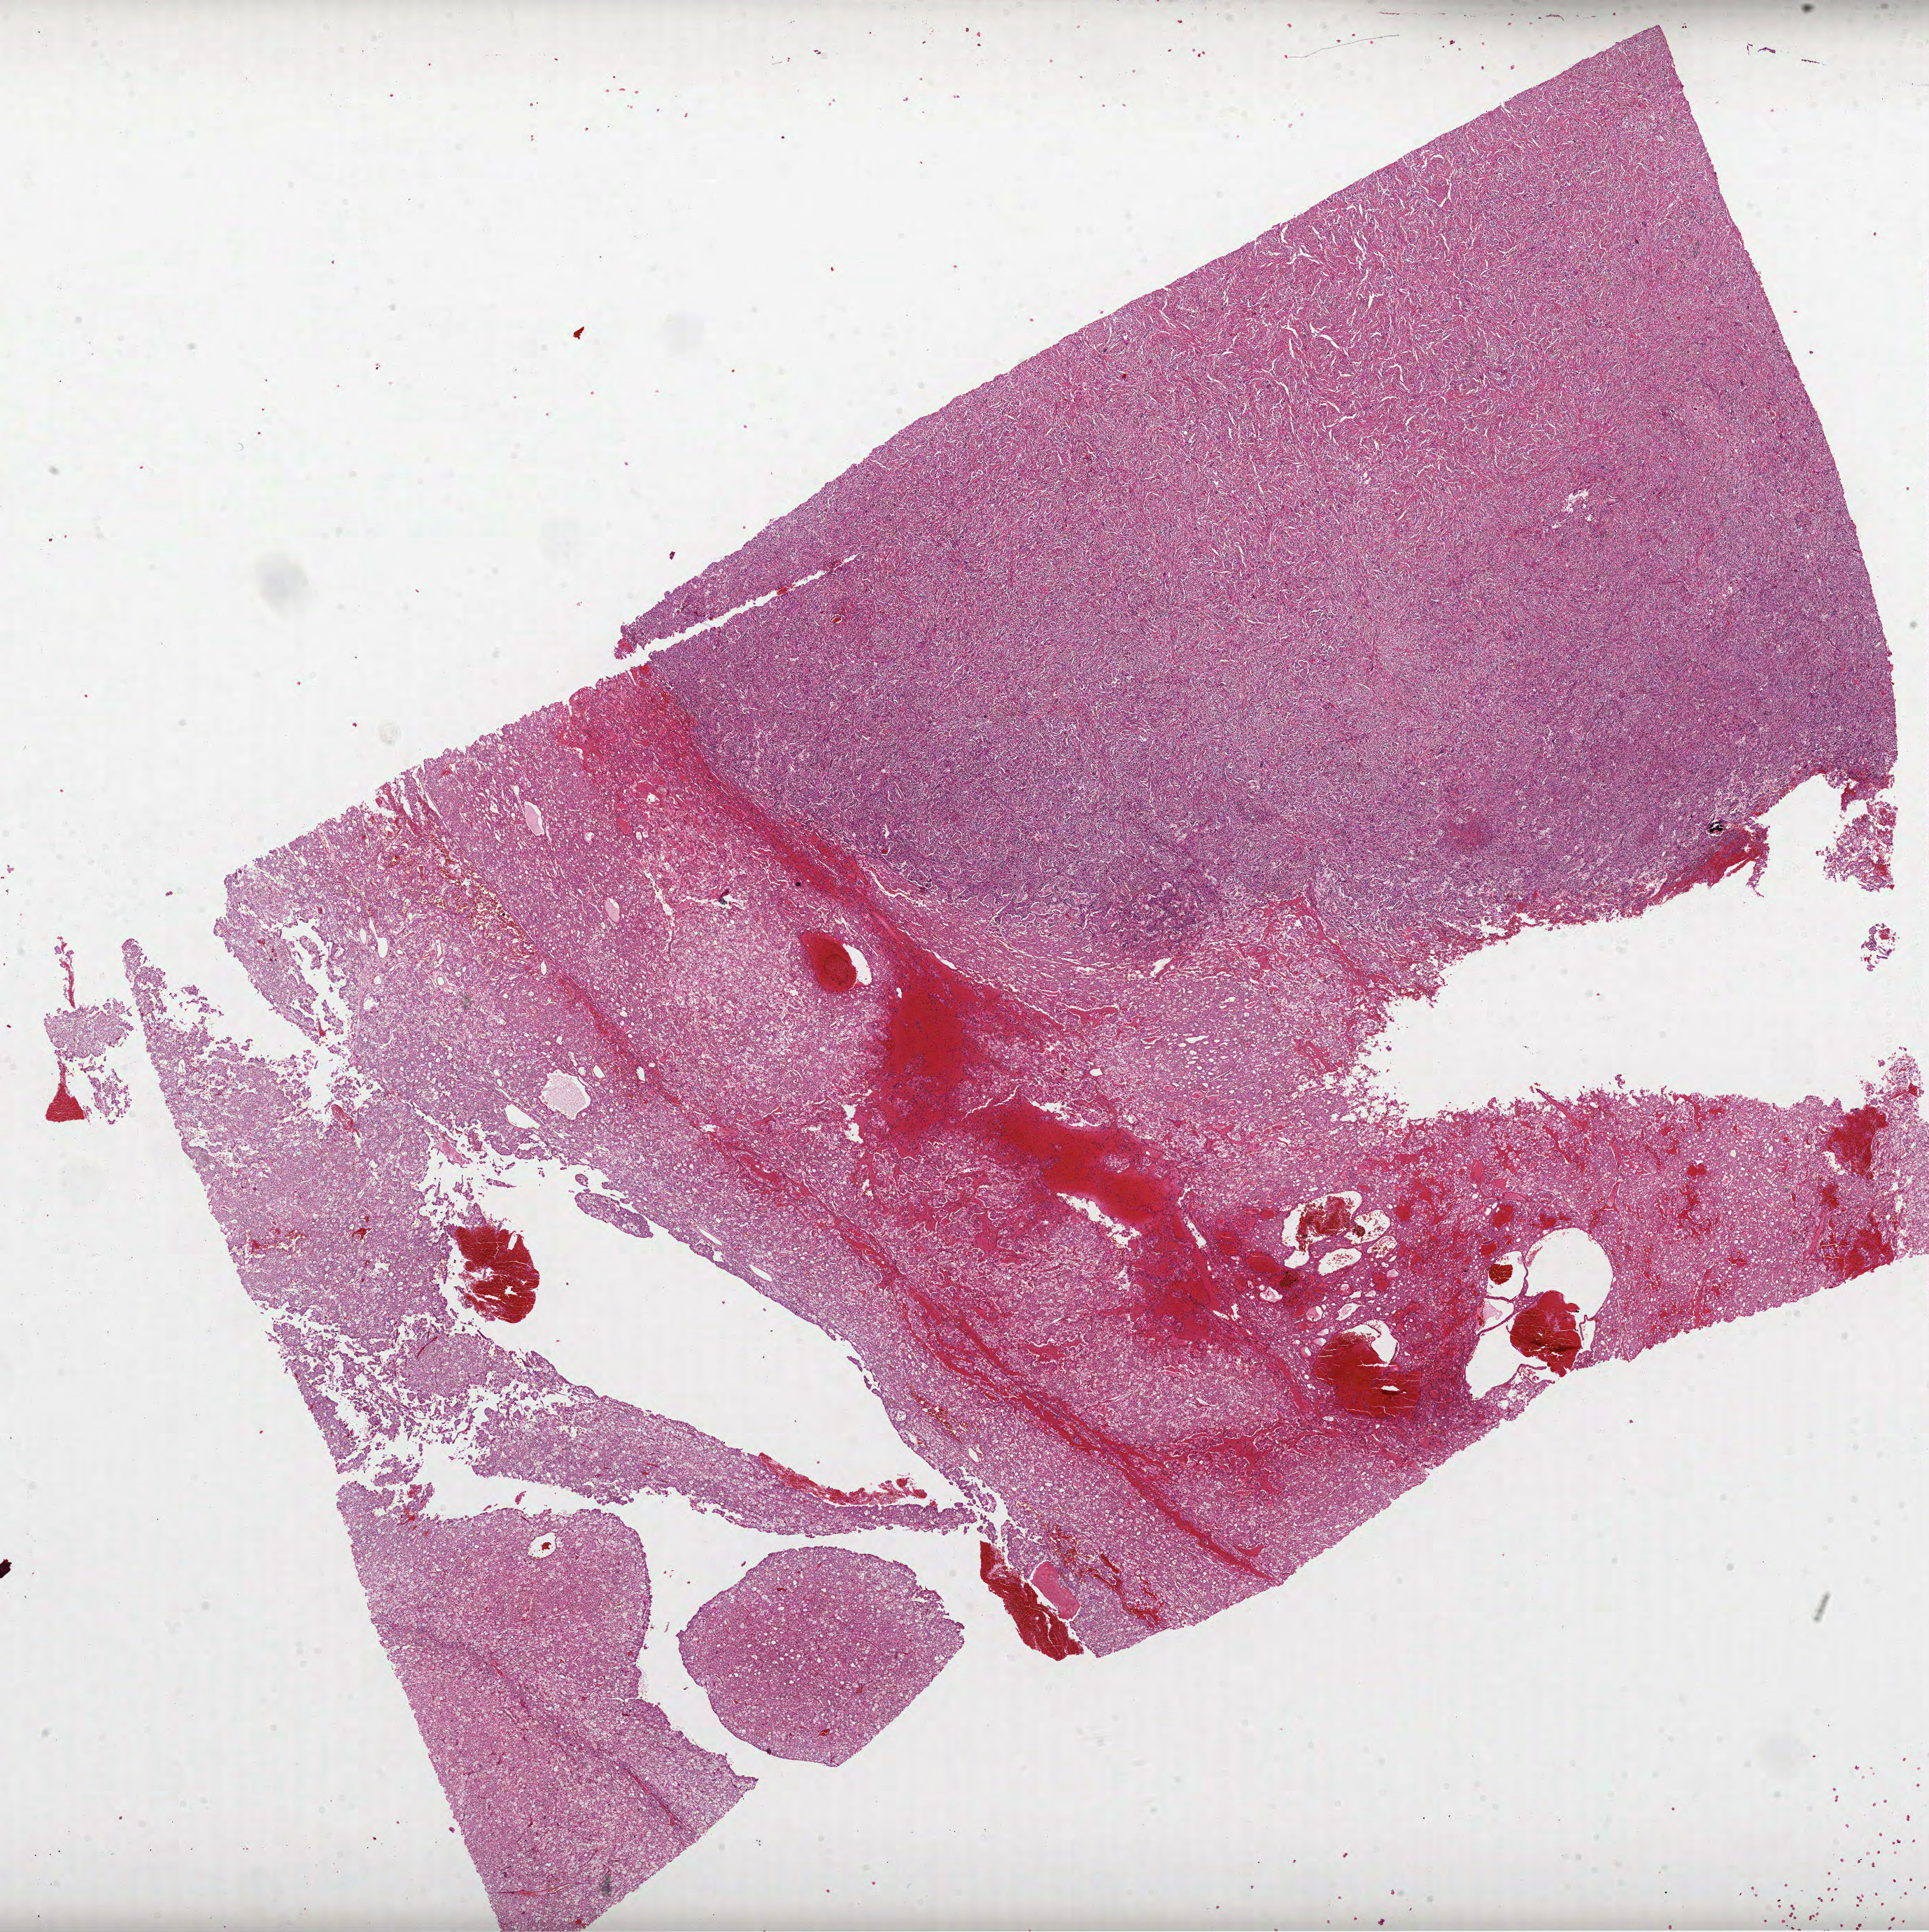
Digitized Hematoxylin and eosin (H&E) stained tissue section (whole slide) — low-resolution overview of the scanned area, about 22.2 x 22.3 mm (from a 40x scan). Formalin-fixed paraffin-embedded (FFPE) diagnostic section. Sample: primary tumour, kidney. Male patient; age at initial diagnosis 58 years. Histologic grade: G3 (poorly differentiated).
AJCC pathologic stage: III. TNM: T3a N0 M0. Diagnosis: Clear cell adenocarcinoma, NOS.